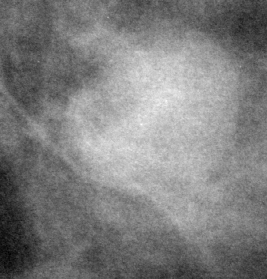
Crop from a digitized film mammogram around one marked abnormality, right breast, CC view.
Finding: mass, shape oval, margins circumscribed; BI-RADS assessment category 3; pathology (as recorded): benign.